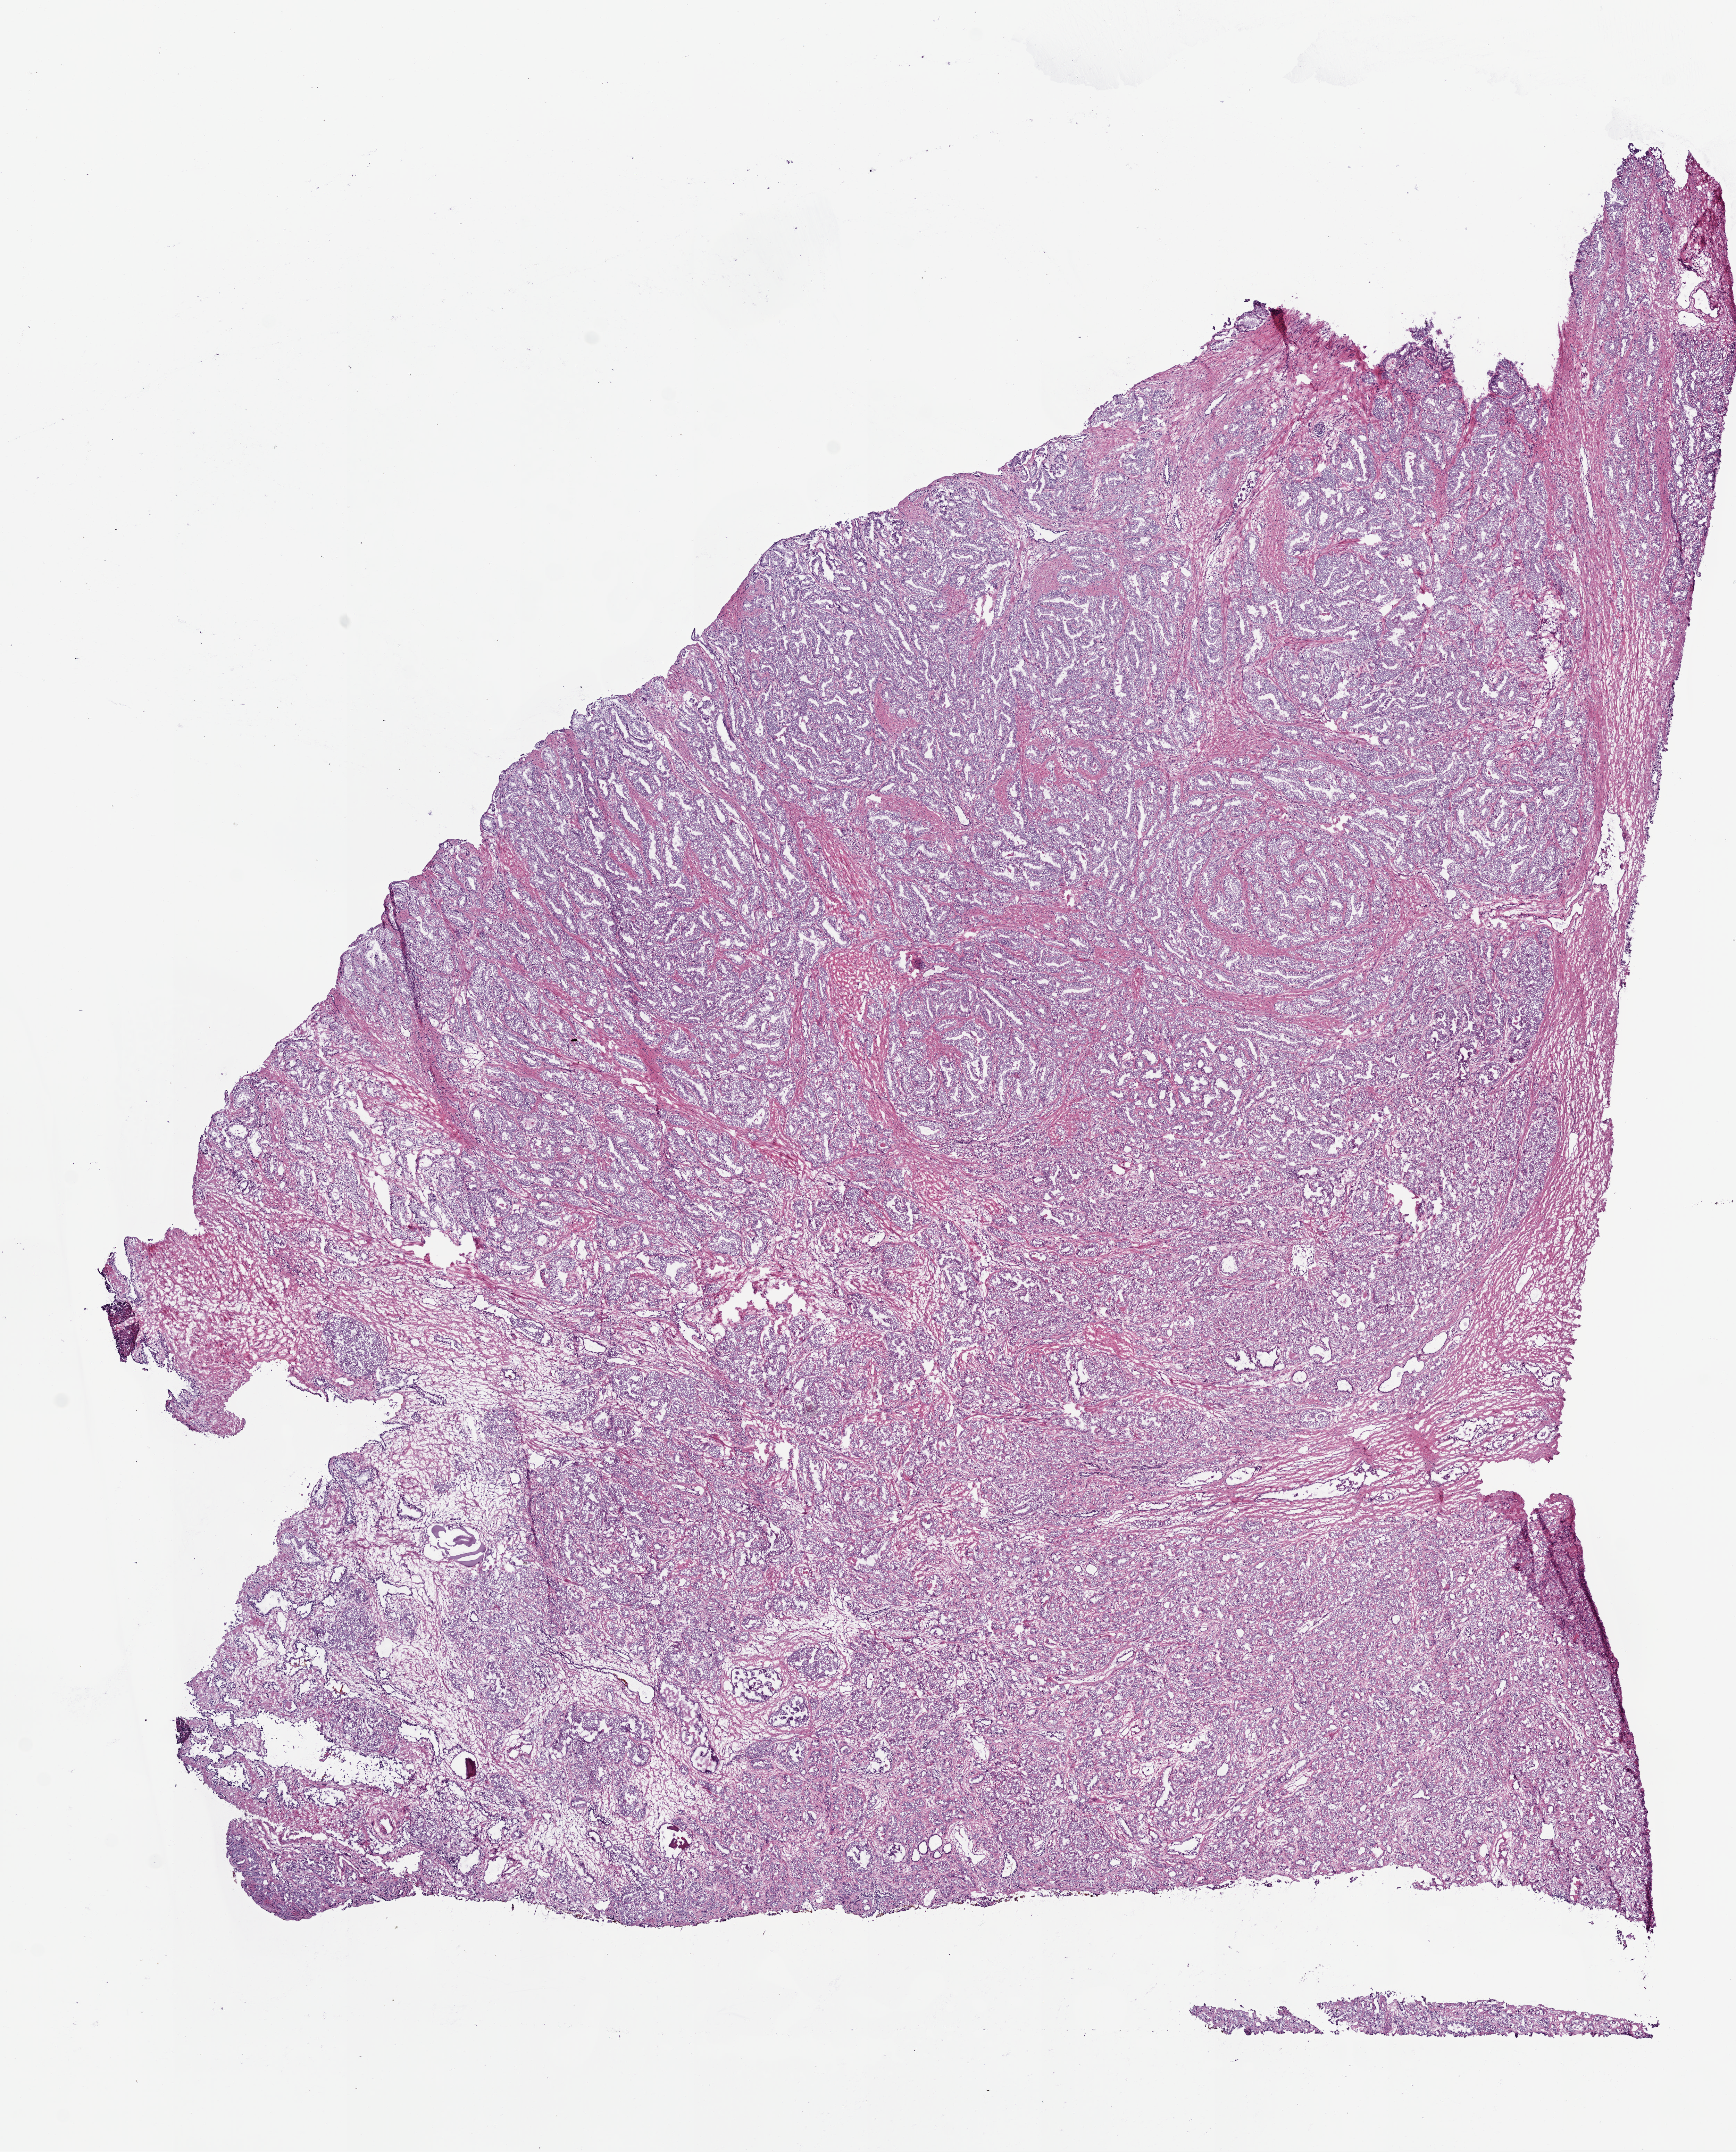
H&E-stained whole-slide image, a low-resolution overview of the entire scanned area, about 10.0 x 12.4 mm (from a 20x scan), frozen section from the top of the tissue portion, prostate, primary tumour sample. Patient: male, age at initial diagnosis 65 years.
Diagnosis: Acinar cell carcinoma (prostate gland).